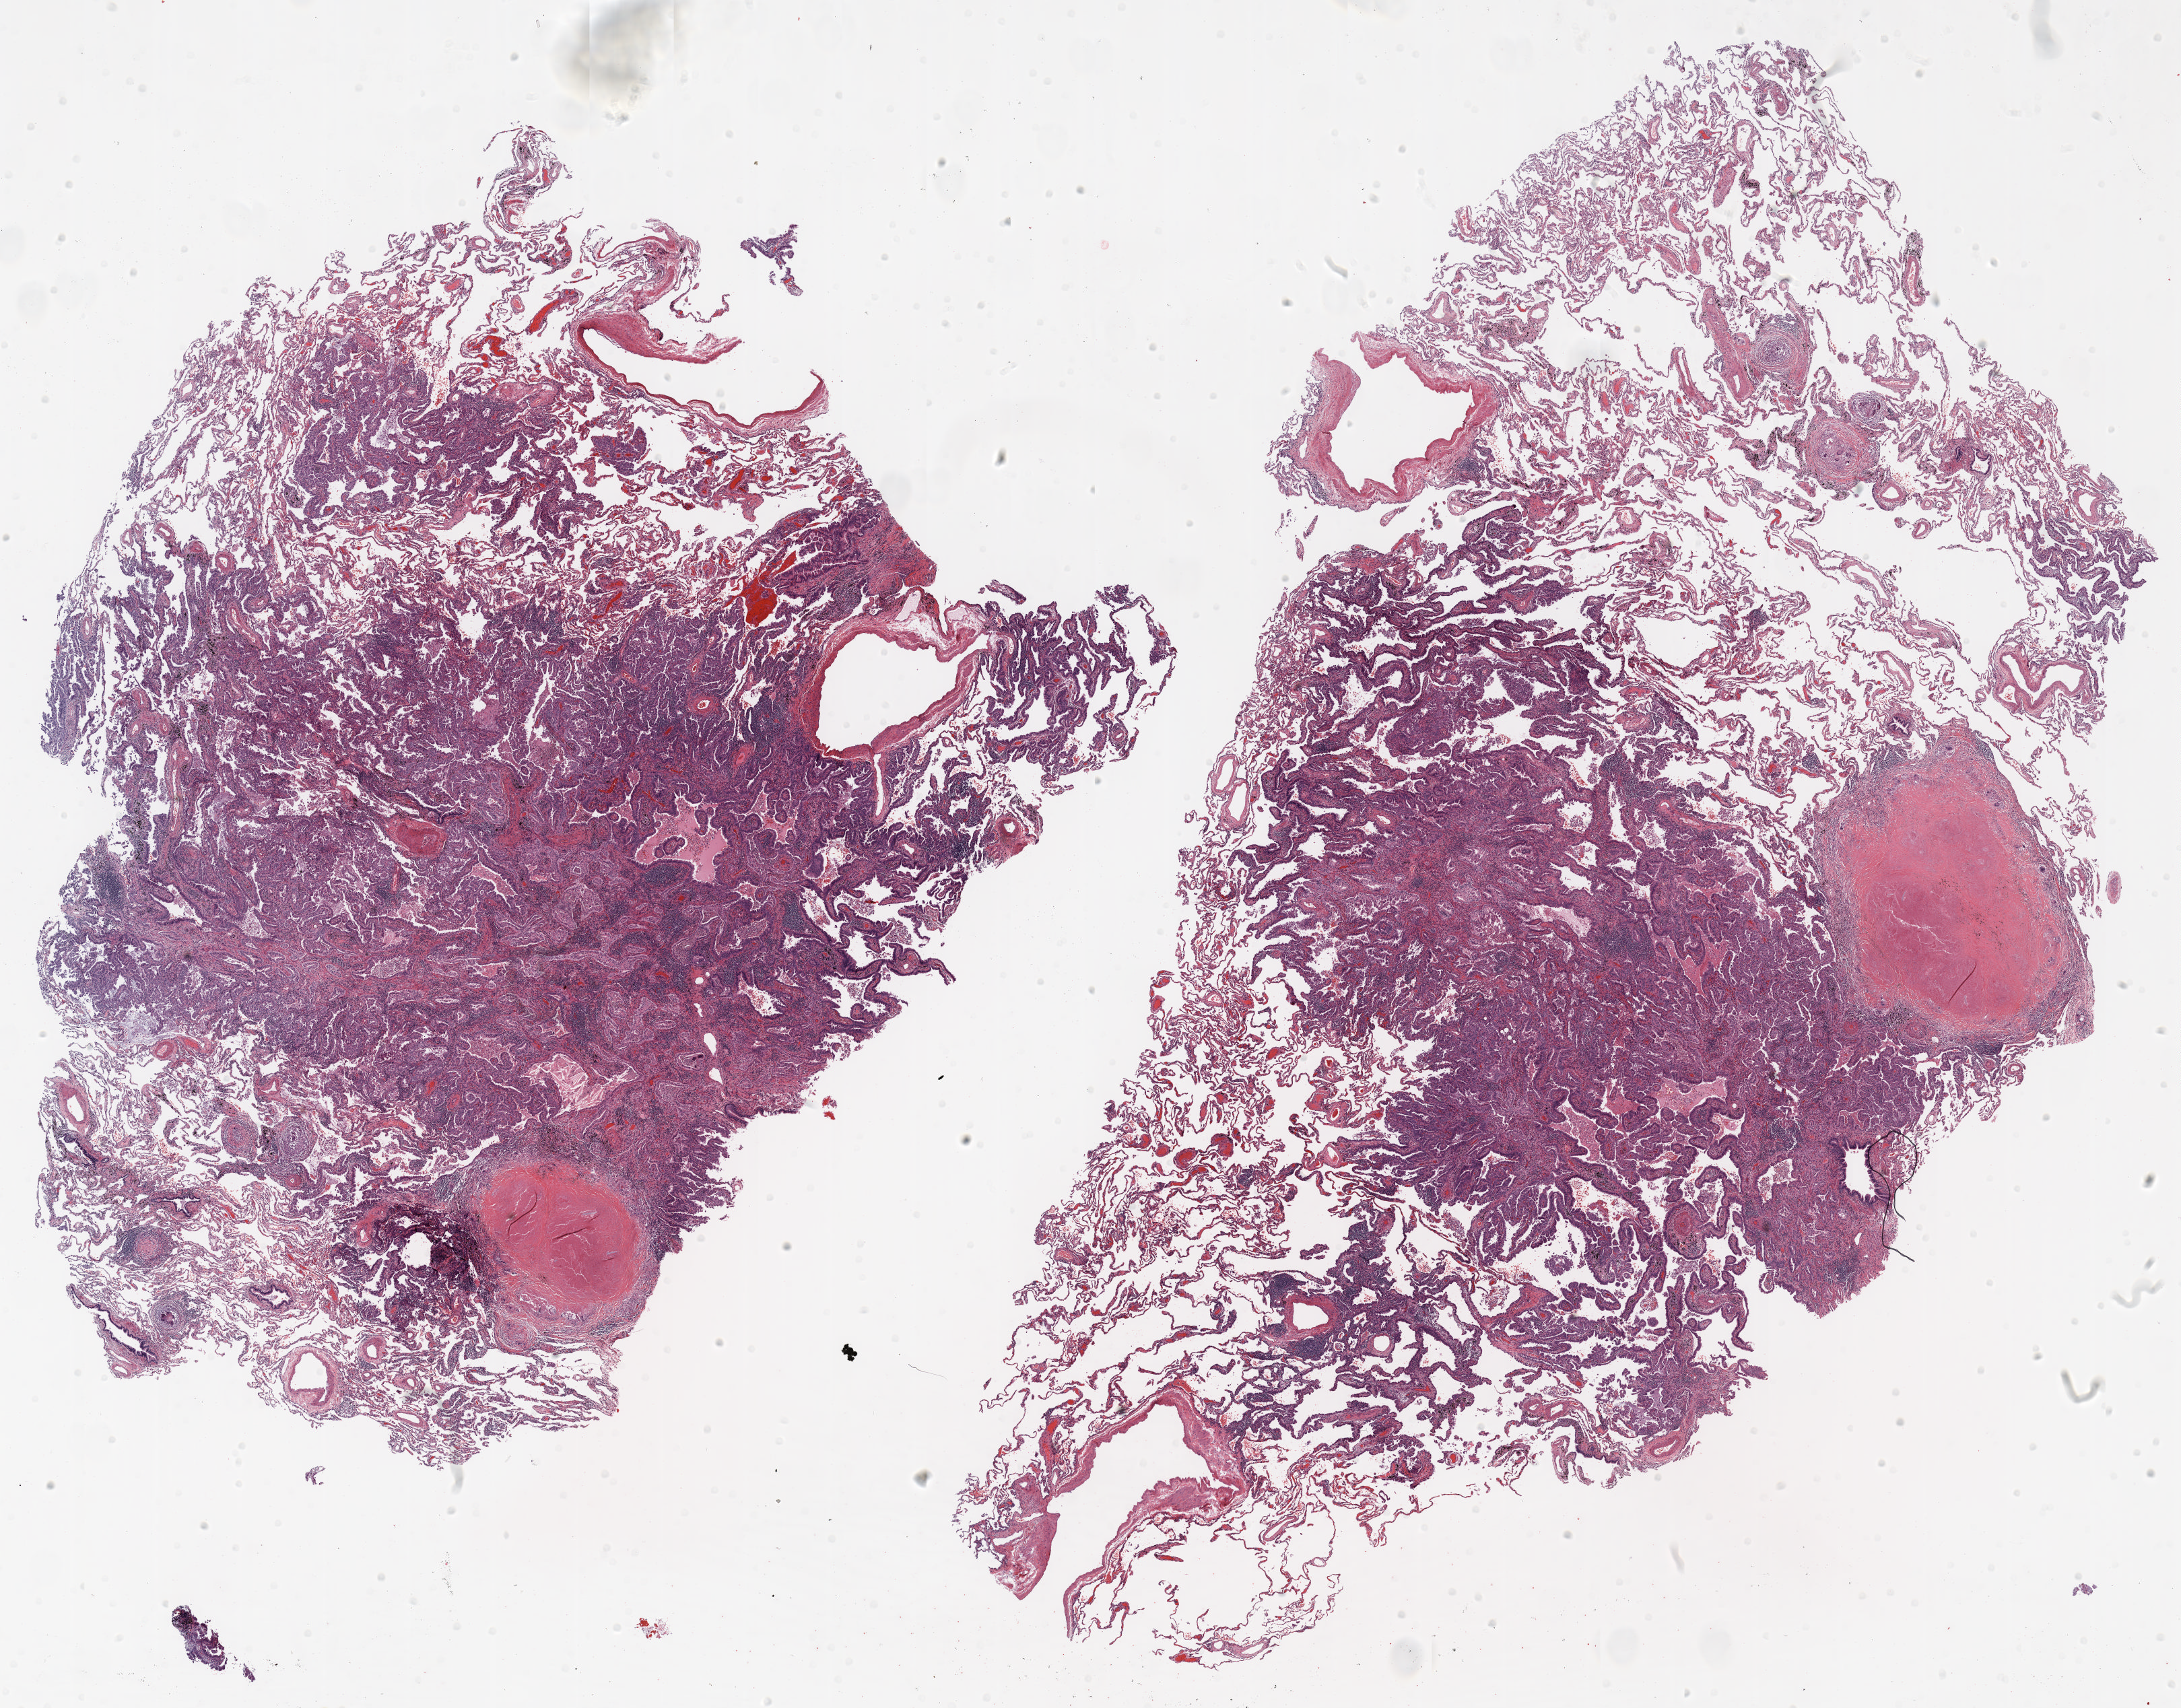
Whole-slide histology image, H&E, shown as a low-resolution overview of the whole scanned area (about 26.0 x 20.4 mm, slide scanned at 20x); FFPE section; lung tissue. Female patient, aged 57 at enrolment. Grade: moderately differentiated (G2).
Primary tumour location (clinical record): left upper lobe. Tumour size (pathology): 19 mm. Participant's lung-cancer diagnosis: Adenocarcinoma with mixed subtypes. Stage (AJCC 6th edition): IIIB.